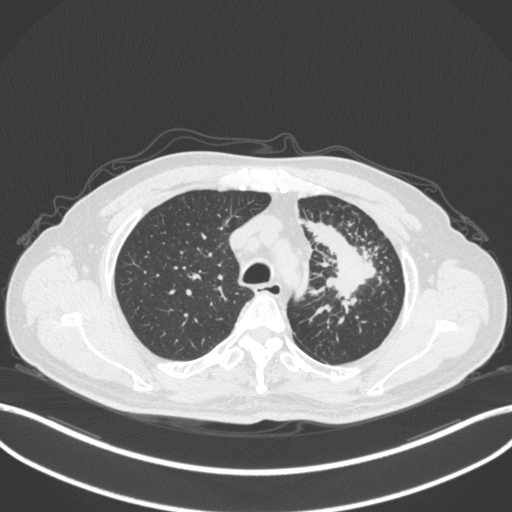
Chest CT, one axial slice. Slice 276 of 386 in the series (ordered by position). Lung window (W 1500 / L -600 HU). 1 mm slice thickness. 512 × 512 image matrix, field of view 400 × 400 mm. Patient: male, 69 years. From the clinical record (not read from this slice): clinical TNM (as recorded): T2a N2 M0.
Annotated regions visible in this slice (rectangle marked by the reading radiologist):
- lung tumour (recorded histology: adenocarcinoma): bounding box [x1, y1, x2, y2] px = [310, 221, 386, 300]